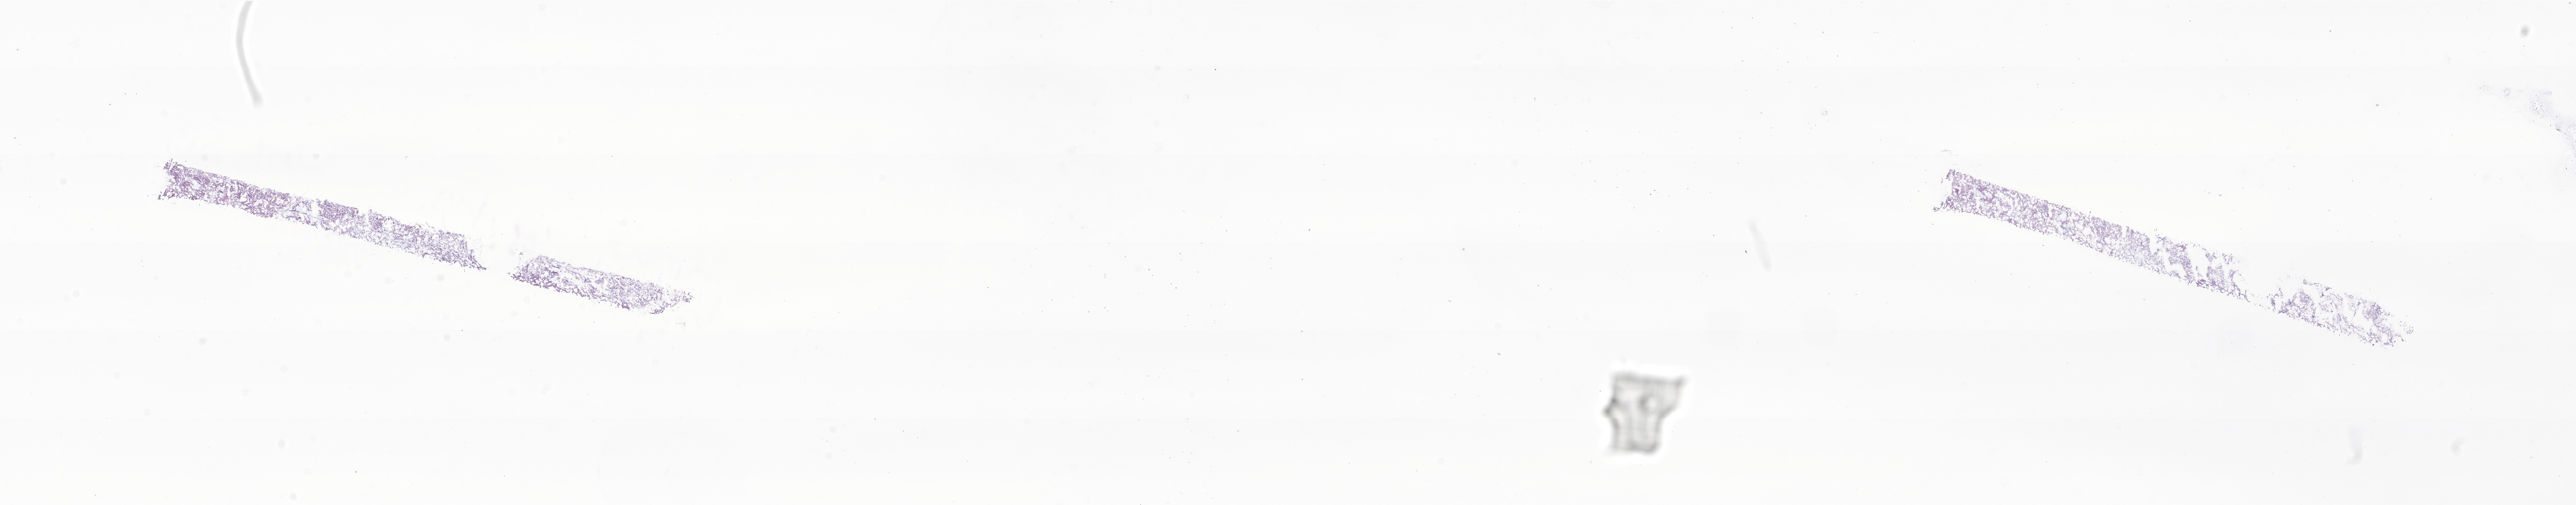
Digitized haematoxylin and eosin-stained section of tumor tissue from the spinal cord, whole scanned area (about 31.2 x 6.1 mm) shown as a low-resolution overview. Cryosection (OCT / tissue freezing medium). Female patient, age 157 months (13 years 1 month).
Recorded diagnosis: Myxopapillary ependymoma.